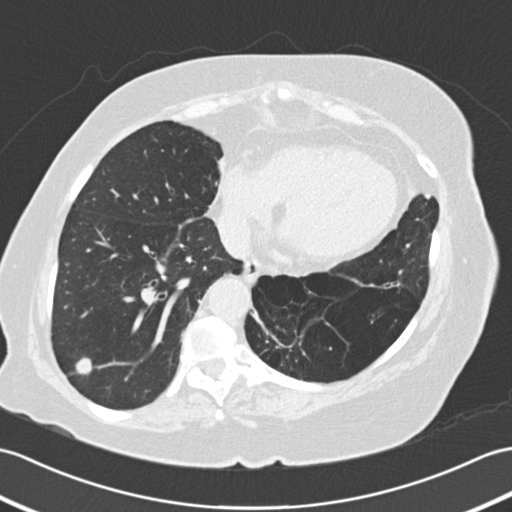
Low-dose screening chest CT, one axial slice; slice 60 of 161 in the series (ordered by position); reconstruction kernel B30f; 120 kVp; lung window (W 1500 / L -600 HU); 2 mm slice thickness; 512 × 512 image matrix, field of view 353 × 353 mm.
Annotated regions visible in this slice (outlined manually by an expert reader):
- lesion 1 (tumor, lower lobe of right lung): box from (x=76, y=358) to (x=92, y=374) px